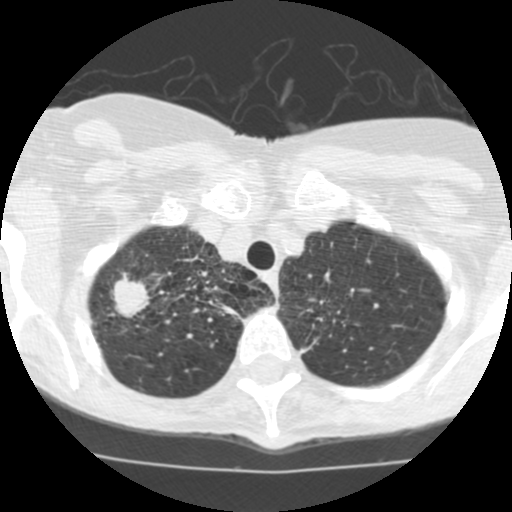
Low-dose screening chest CT, one axial slice. Position 98 of 115 along the scan axis. 120 kVp. Lung window (W 1500 / L -600 HU). 512 × 512 image matrix, field of view 280 × 280 mm.
Annotated regions visible in this slice (manually delineated by an expert):
- lesion 1 (tumor, upper lobe of right lung): bounding box (x1, y1, x2, y2) in pixels: (113, 273, 148, 318)